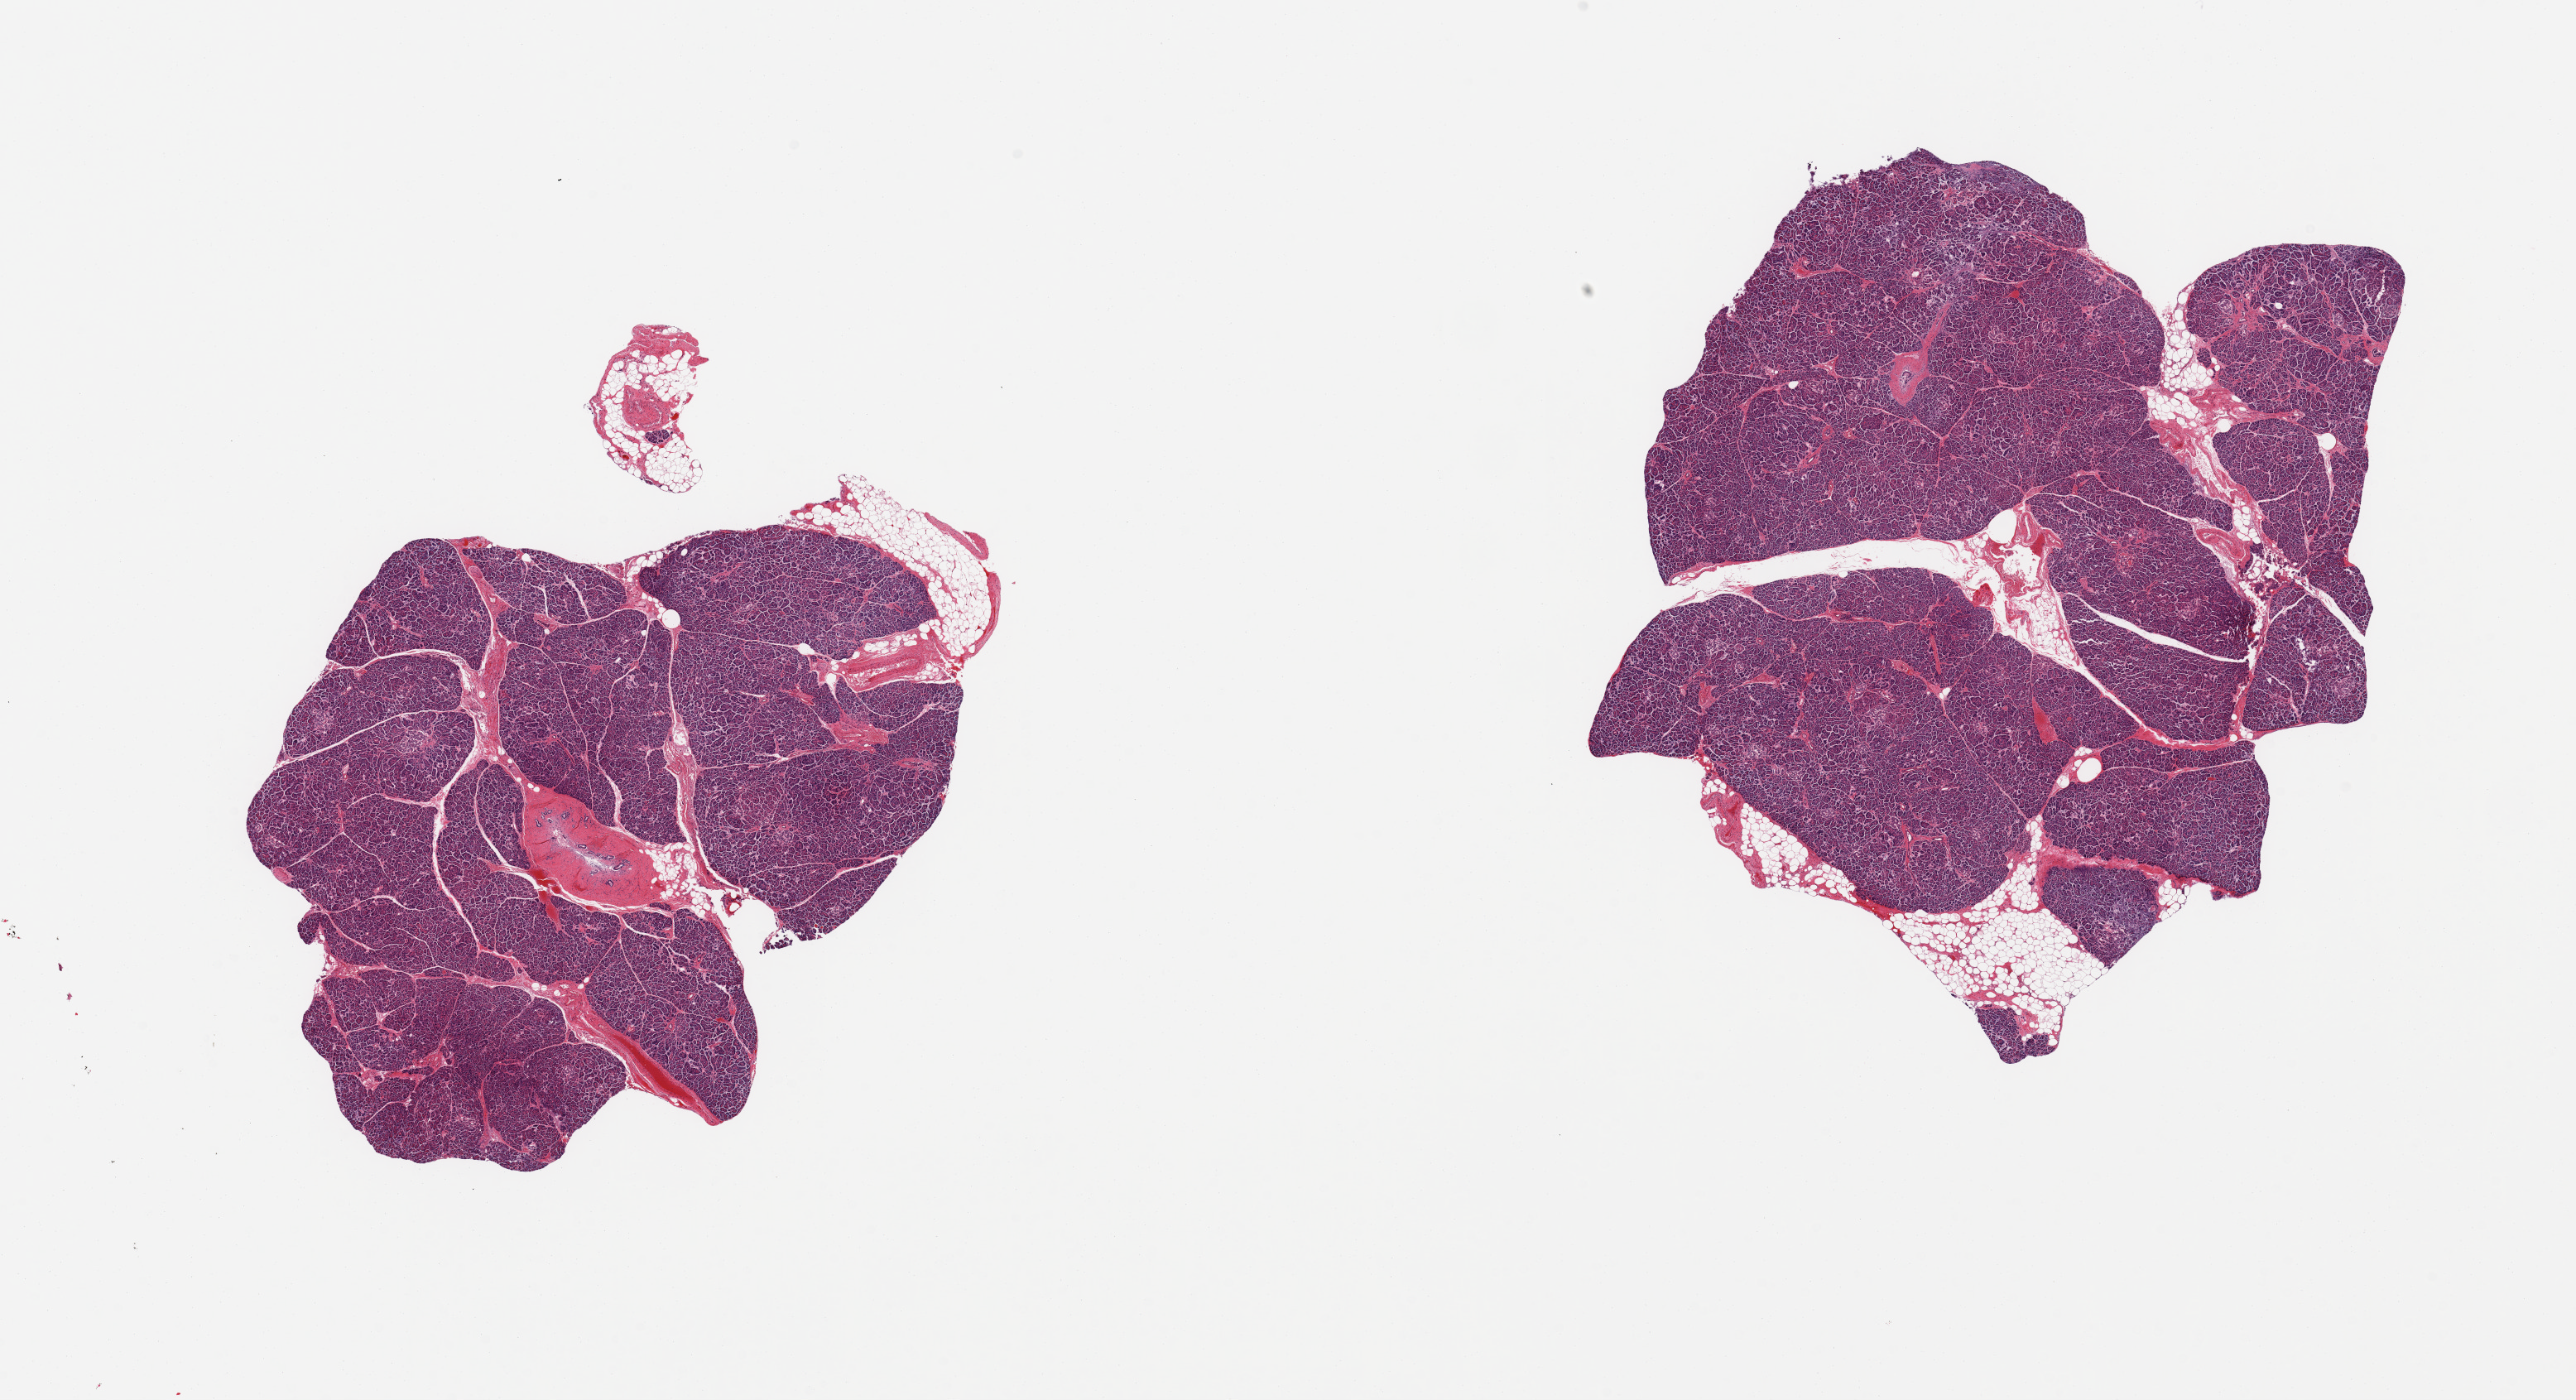
Digitized H&E-stained section — whole scanned area (about 24.6 x 13.4 mm, slide scanned at 20x) shown as a low-resolution overview, PAXgene-fixed, paraffin-embedded tissue, section of pancreas (target tissue), tissue donor sample. Male donor.
Reviewer comment on this tissue sample: 2 pieces, moderate advanced saponification; Islets visible, early degenerative changes.